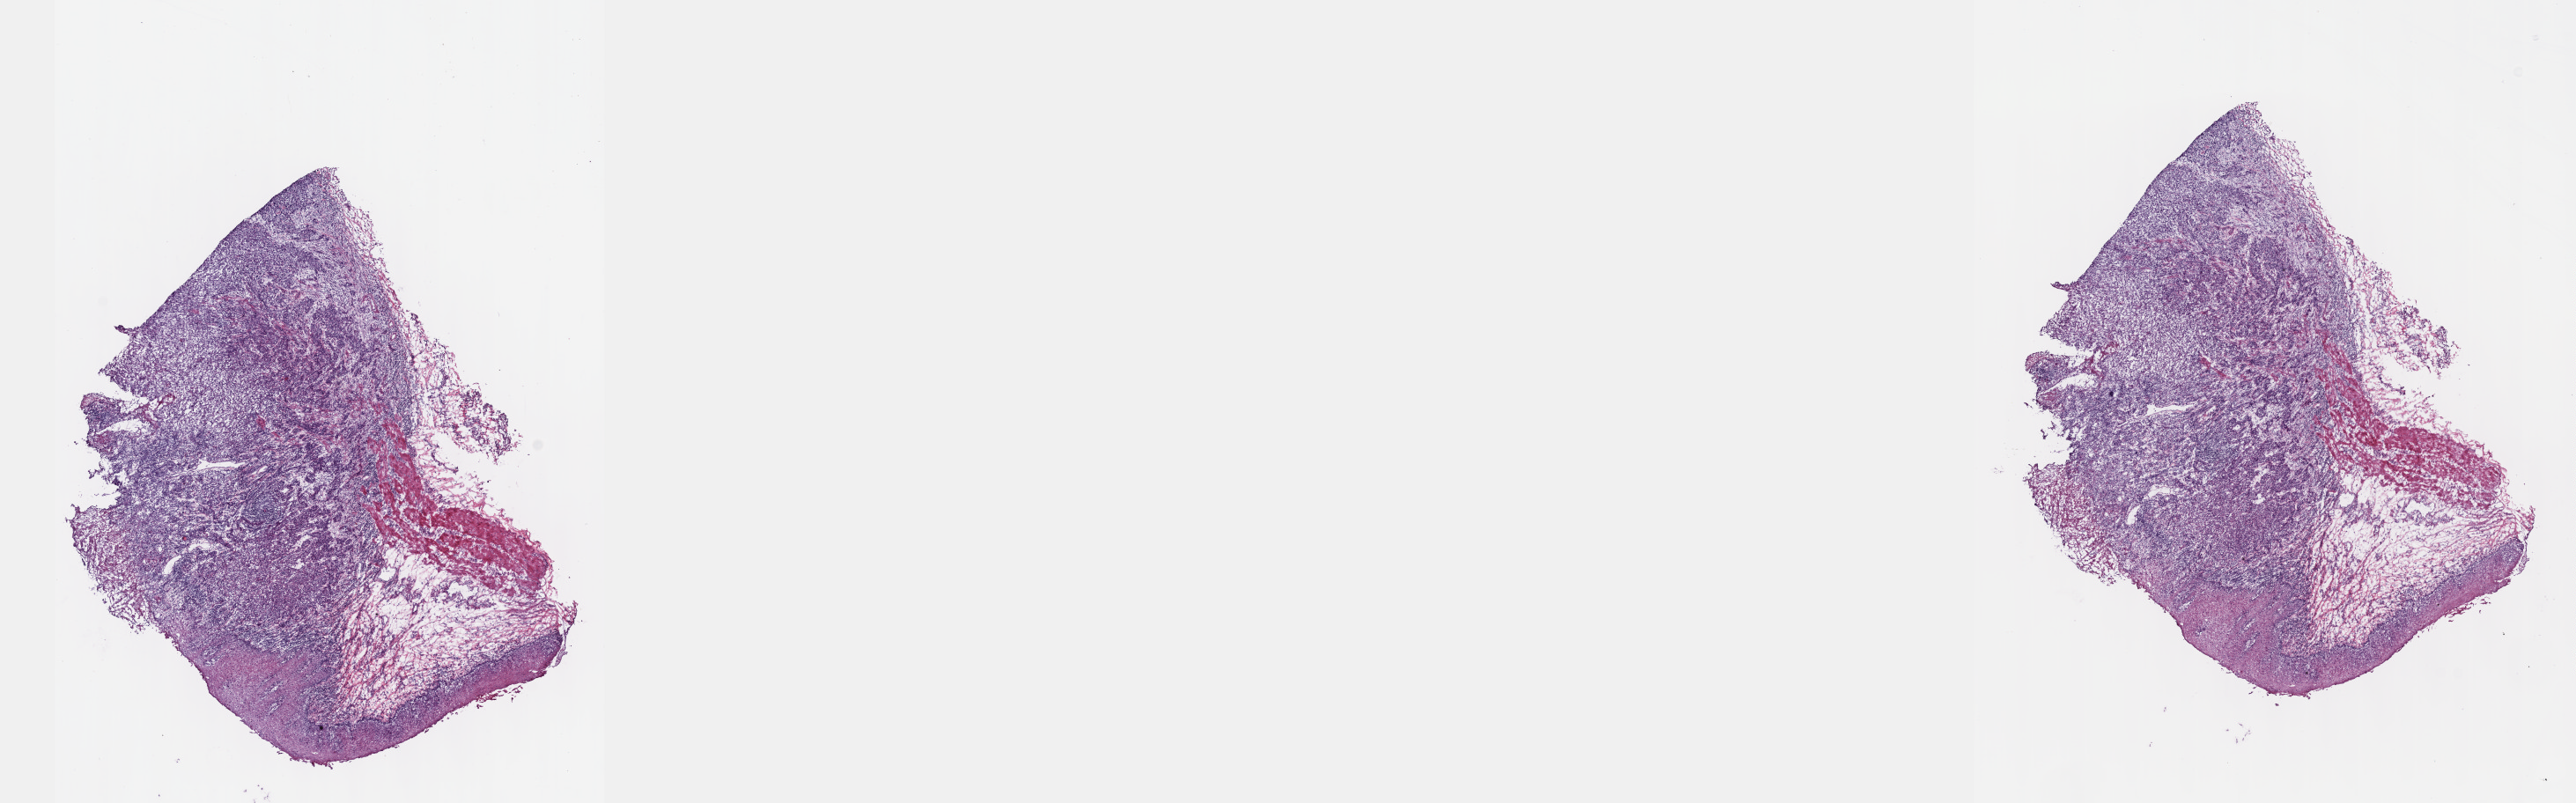
Whole-slide histology image, H&E — a low-resolution overview of the entire scanned area, about 23.6 x 7.4 mm; frozen section from the top of the tissue portion; sample: primary tumour, esophagus. Male patient; age at initial diagnosis 71 years. Histologic grade: G3 (poorly differentiated). Composition of this section per pathologist review: tumour cells 70%, tumour nuclei 80%, normal cells 30%, stromal cells 0%, necrosis 0%. Infiltration values recorded for this section: lymphocyte infiltration 0%, monocyte infiltration 0%, neutrophil infiltration 0%.
* AJCC pathologic stage: IIA (5th edition)
* pathologic diagnosis: Squamous cell carcinoma, NOS